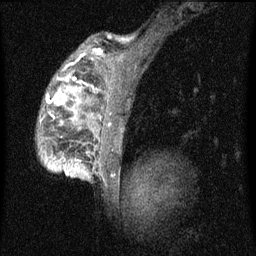
Breast MRI (dynamic contrast-enhanced), one sagittal slice; slice 50 of 60 in the series (ordered by position); dynamic contrast-enhanced series, image 2 of 4 at this slice position (ordered by acquisition); 1.5 T; TE 4.2 ms, TR 8 ms; 2 mm slice thickness; 256 × 256 image matrix. Patient: female, 50 years.
Structures marked on this image (semi-automatic segmentation, software-assisted and operator-edited):
- analysis volume of interest (the breast-tissue region the enhancement analysis was run in; not a lesion): bounding box [x1, y1, x2, y2] px = [38, 46, 124, 177]
- tumour enhancement mask (voxels above the 70 % enhancement threshold inside the analysis volume of interest): [47, 76, 95, 115]